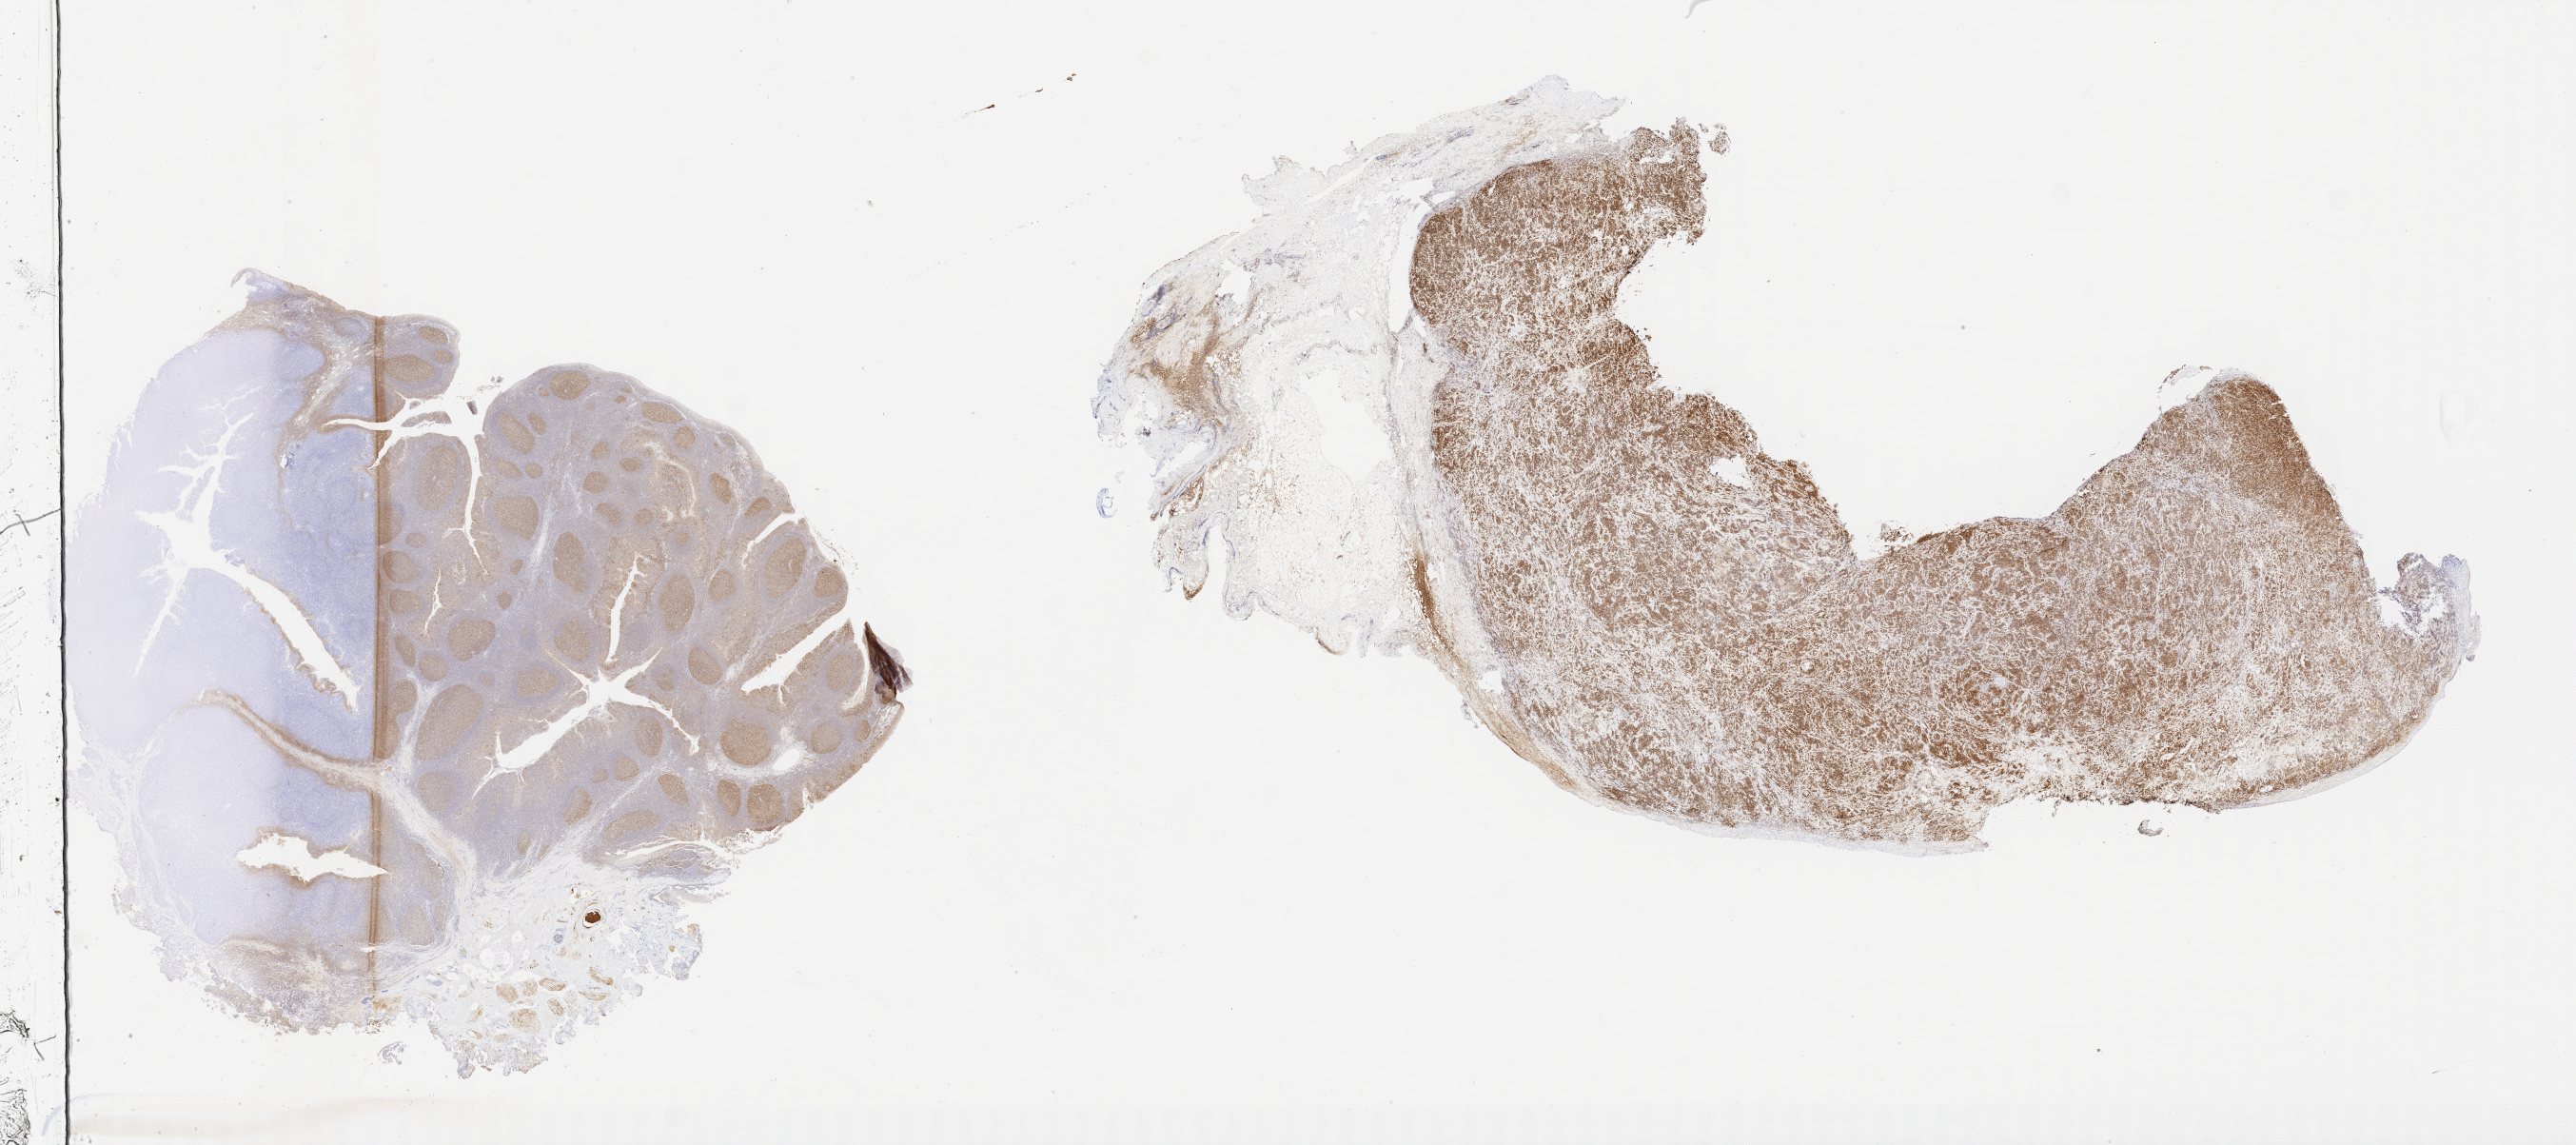
IHC for BCL6, whole-slide image, shown as a low-resolution overview of the whole scanned area (about 43.8 x 19.5 mm). Specimen: tumor tissue. Site: bone. Male patient, aged 48.
- histologic diagnosis: Diffuse large B-cell lymphoma, NOS